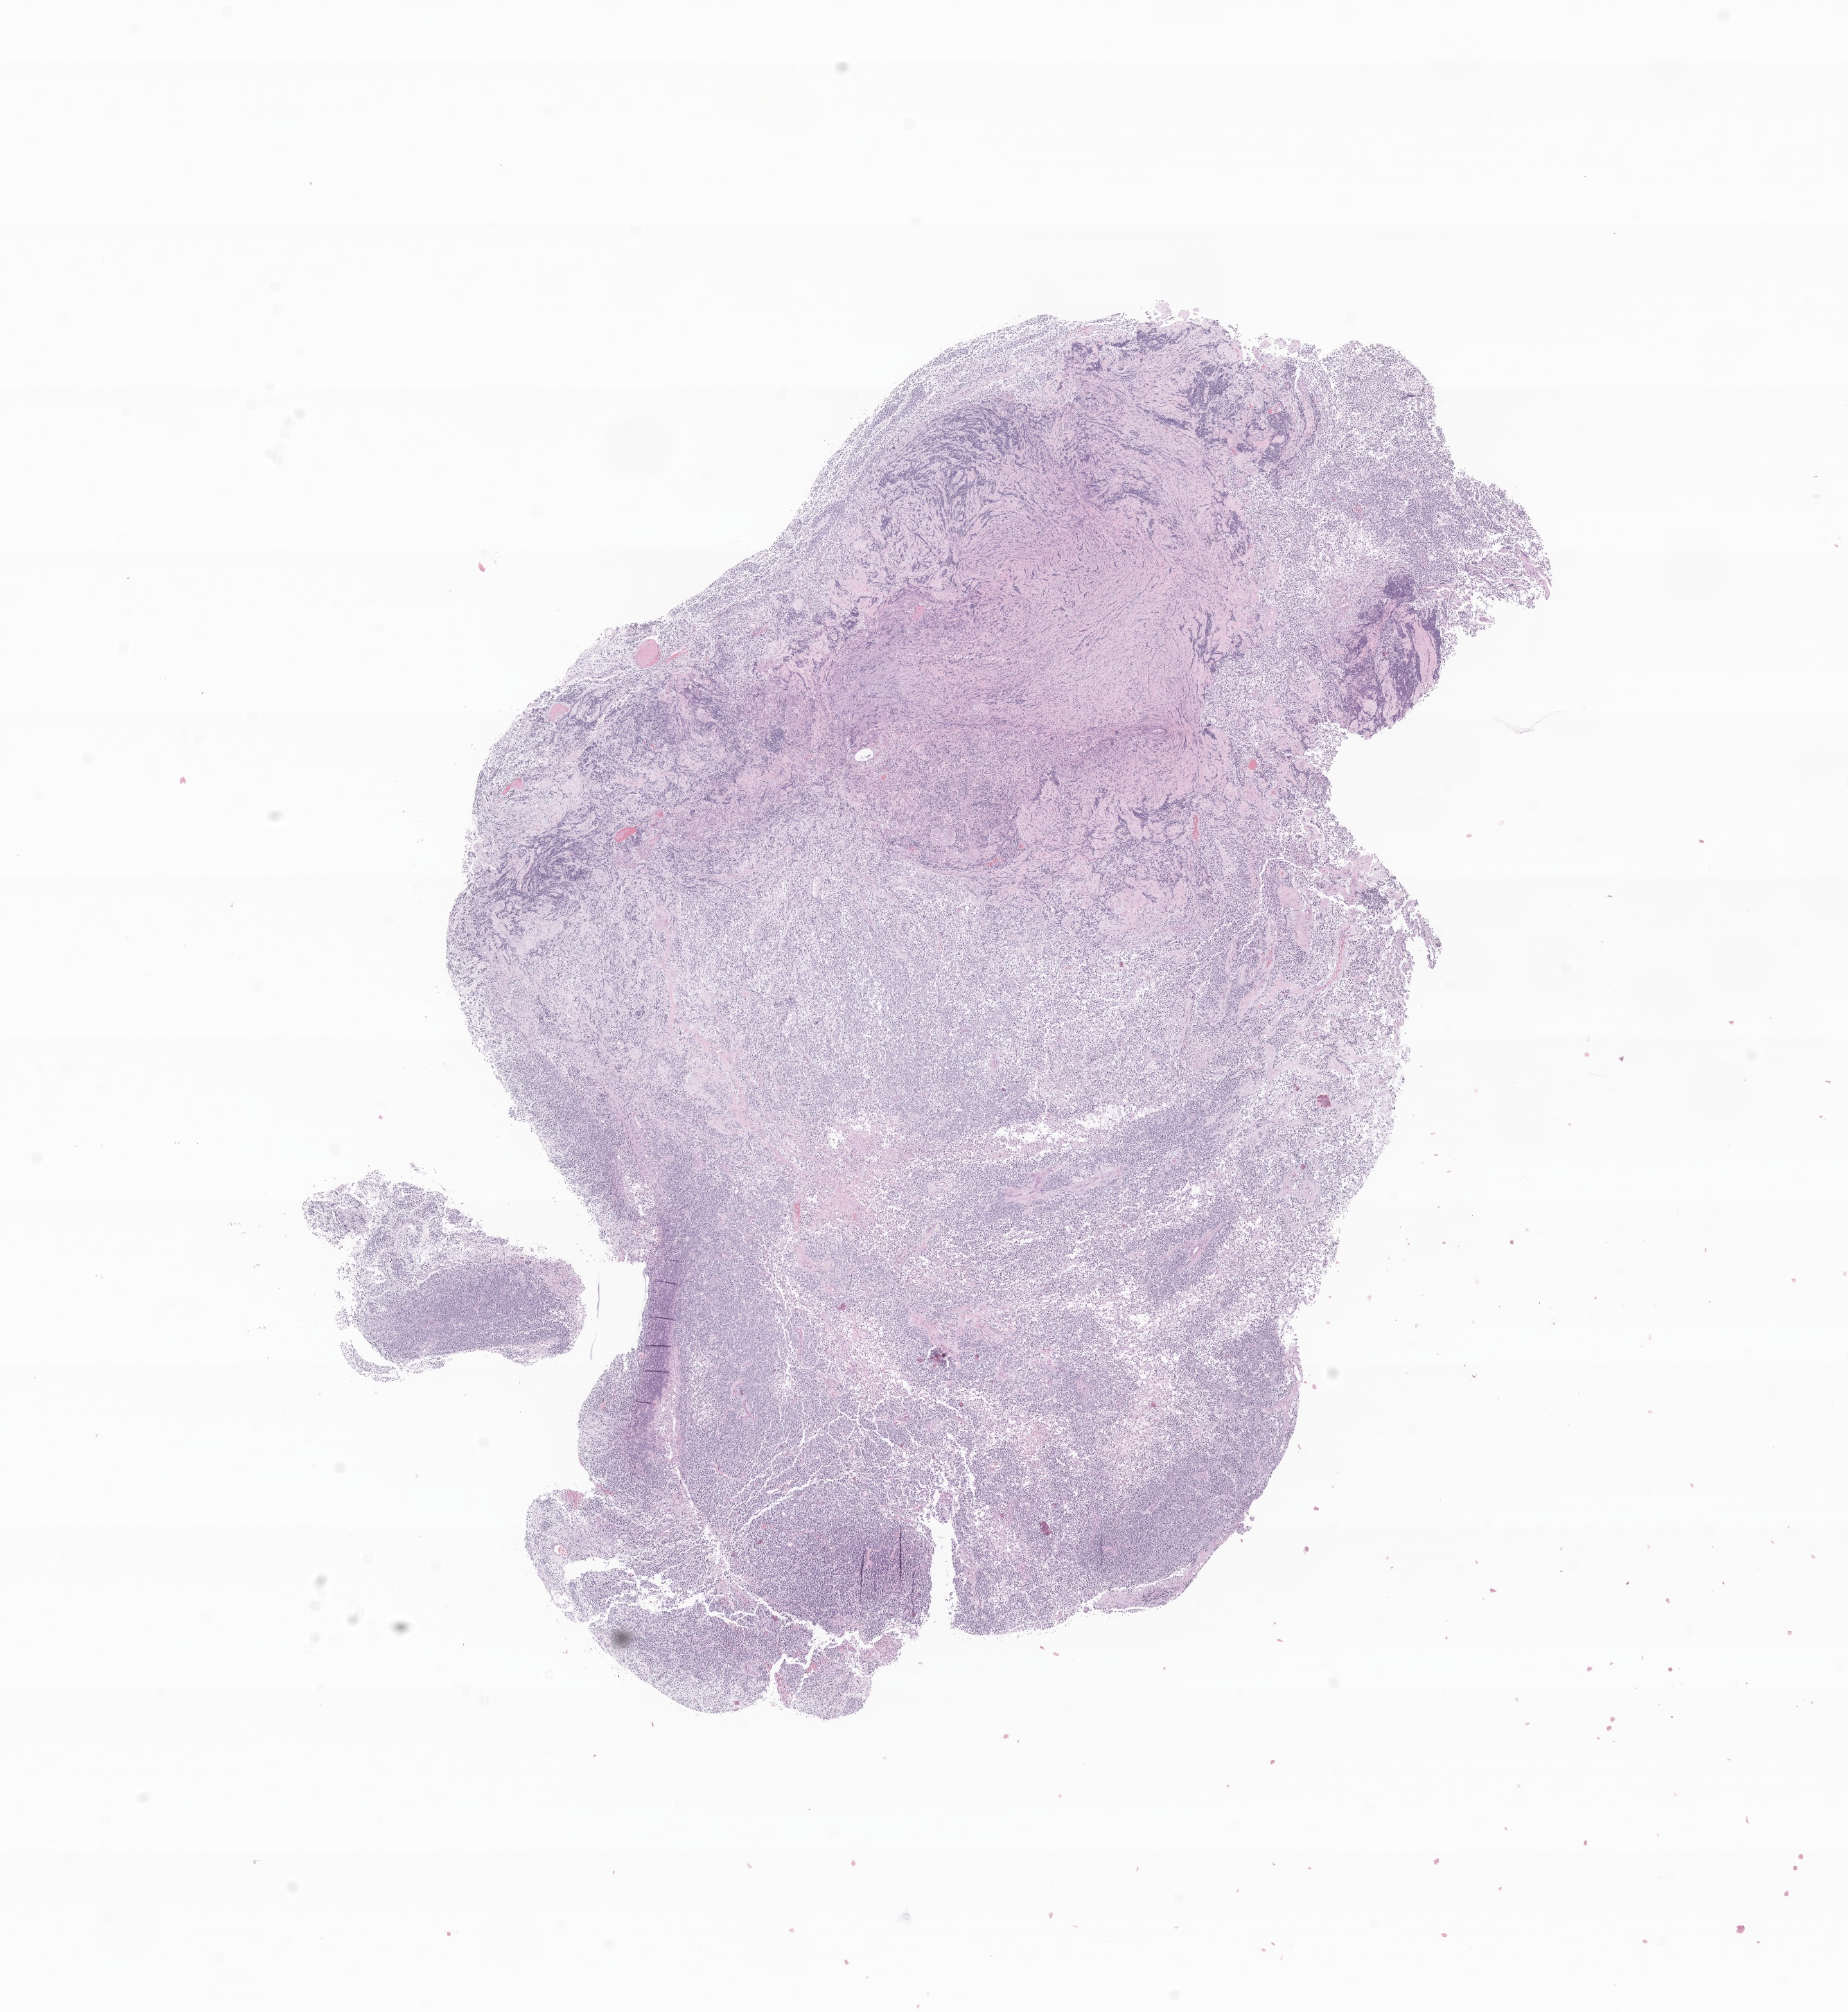
Whole-slide image, haematoxylin and eosin stain of tumor tissue from the brain — low-resolution overview of the scanned area, about 12.1 x 13.2 mm, FFPE section. Patient: male, age 37 months.
Diagnosis (ICD-O-3 morphology term): Glioma, malignant.